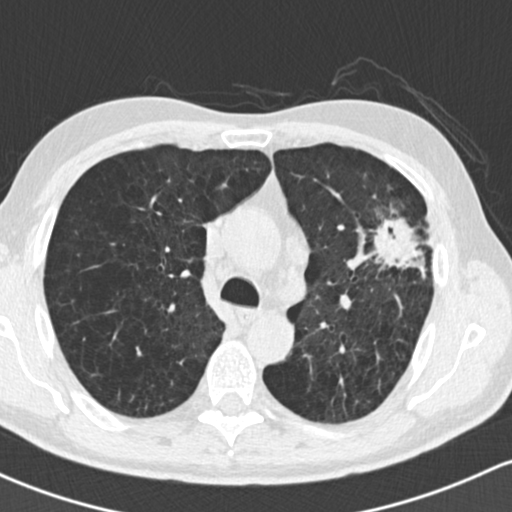
Axial slice from a low-dose chest CT screening exam, baseline annual screen, lung window (W 1500 / L -600 HU), 2 mm slice thickness, standard (soft-tissue) reconstruction kernel (B30f), slice 57 of 162 in the series. Male participant, aged 61 years at enrolment. Former smoker at enrolment.
Expert-annotated lung lesion, bounding box <354,185,449,291> (left, top, right, bottom; pixels). Reader record for this screening exam (exam-level; its link to the box is not recorded): non-calcified nodule or mass ≥4 mm, left upper lobe, 35 × 35 mm, spiculated (stellate) margins, soft tissue attenuation. Later outcome: lung cancer diagnosed 19 days after this screen — adenocarcinoma, NOS, left upper lobe, well differentiated (G1), stage IIIA (AJCC 6th edition), 45 mm at pathology.